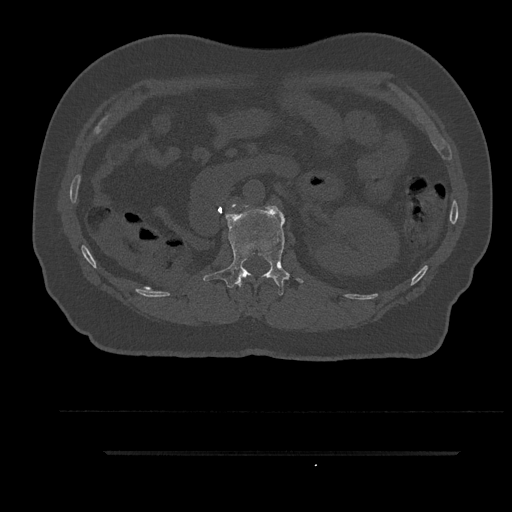
CT including the spine, one axial slice; position 178 of 797 along the scan axis; 120 kVp; bone window (W 1800 / L 400 HU); 0.5 mm slice thickness; 512 × 512 image matrix. Male patient, age 63 years. Case-level facts recorded for this patient, not image findings: primary cancer: renal.
Structures marked on this image (semi-automatic segmentation, software-assisted and operator-edited):
- L1 vertebra: box from (x=203, y=205) to (x=303, y=296) px
- L2 vertebra: (x=232, y=204)–(x=236, y=208)
- T12 vertebra: (x=239, y=282)–(x=242, y=287)